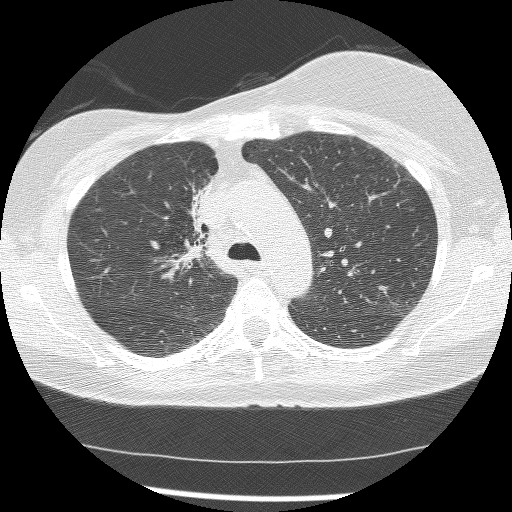
Chest CT (low-dose screening protocol), one axial image. Baseline screening round. Lung window (W 1500 / L -600 HU). 2.5 mm slice thickness. Lung (sharp) reconstruction kernel (BONE). Slice 47 of 172 in the series. Female participant, aged 56 years at enrolment. Current smoker at enrolment.
Lesion marked by an expert reader, bounding box (x1, y1, x2, y2) in pixels: (163, 176, 220, 267). The screening reader recorded 2 non-calcified nodules or masses ≥4 mm on this exam (right lower lobe, right middle lobe); which of them this box marks is not recorded. Participant outcome: lung cancer diagnosed 1185 days after this screen — adenocarcinoma, NOS, right upper lobe, stage IIIB (AJCC 6th edition), 8 mm at pathology.